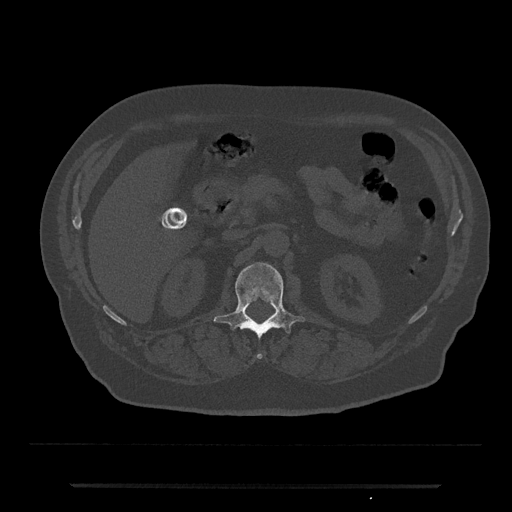
CT including the spine, one axial slice. Position 537 of 797 along the scan axis. Reconstruction kernel Br40s/3. 120 kVp. Bone window (W 1800 / L 400 HU). 0.5 mm slice thickness. 512 × 512 image matrix, field of view 434 × 434 mm. Patient: male, 80 years. Case-level facts recorded for this patient, not image findings: primary cancer: prostate; vertebrae with lytic lesions (as recorded): L1, T11.
Structures marked on this image (semi-automatically segmented with operator editing):
- L1 vertebra: bounding box [x1, y1, x2, y2] px = [214, 262, 304, 359]